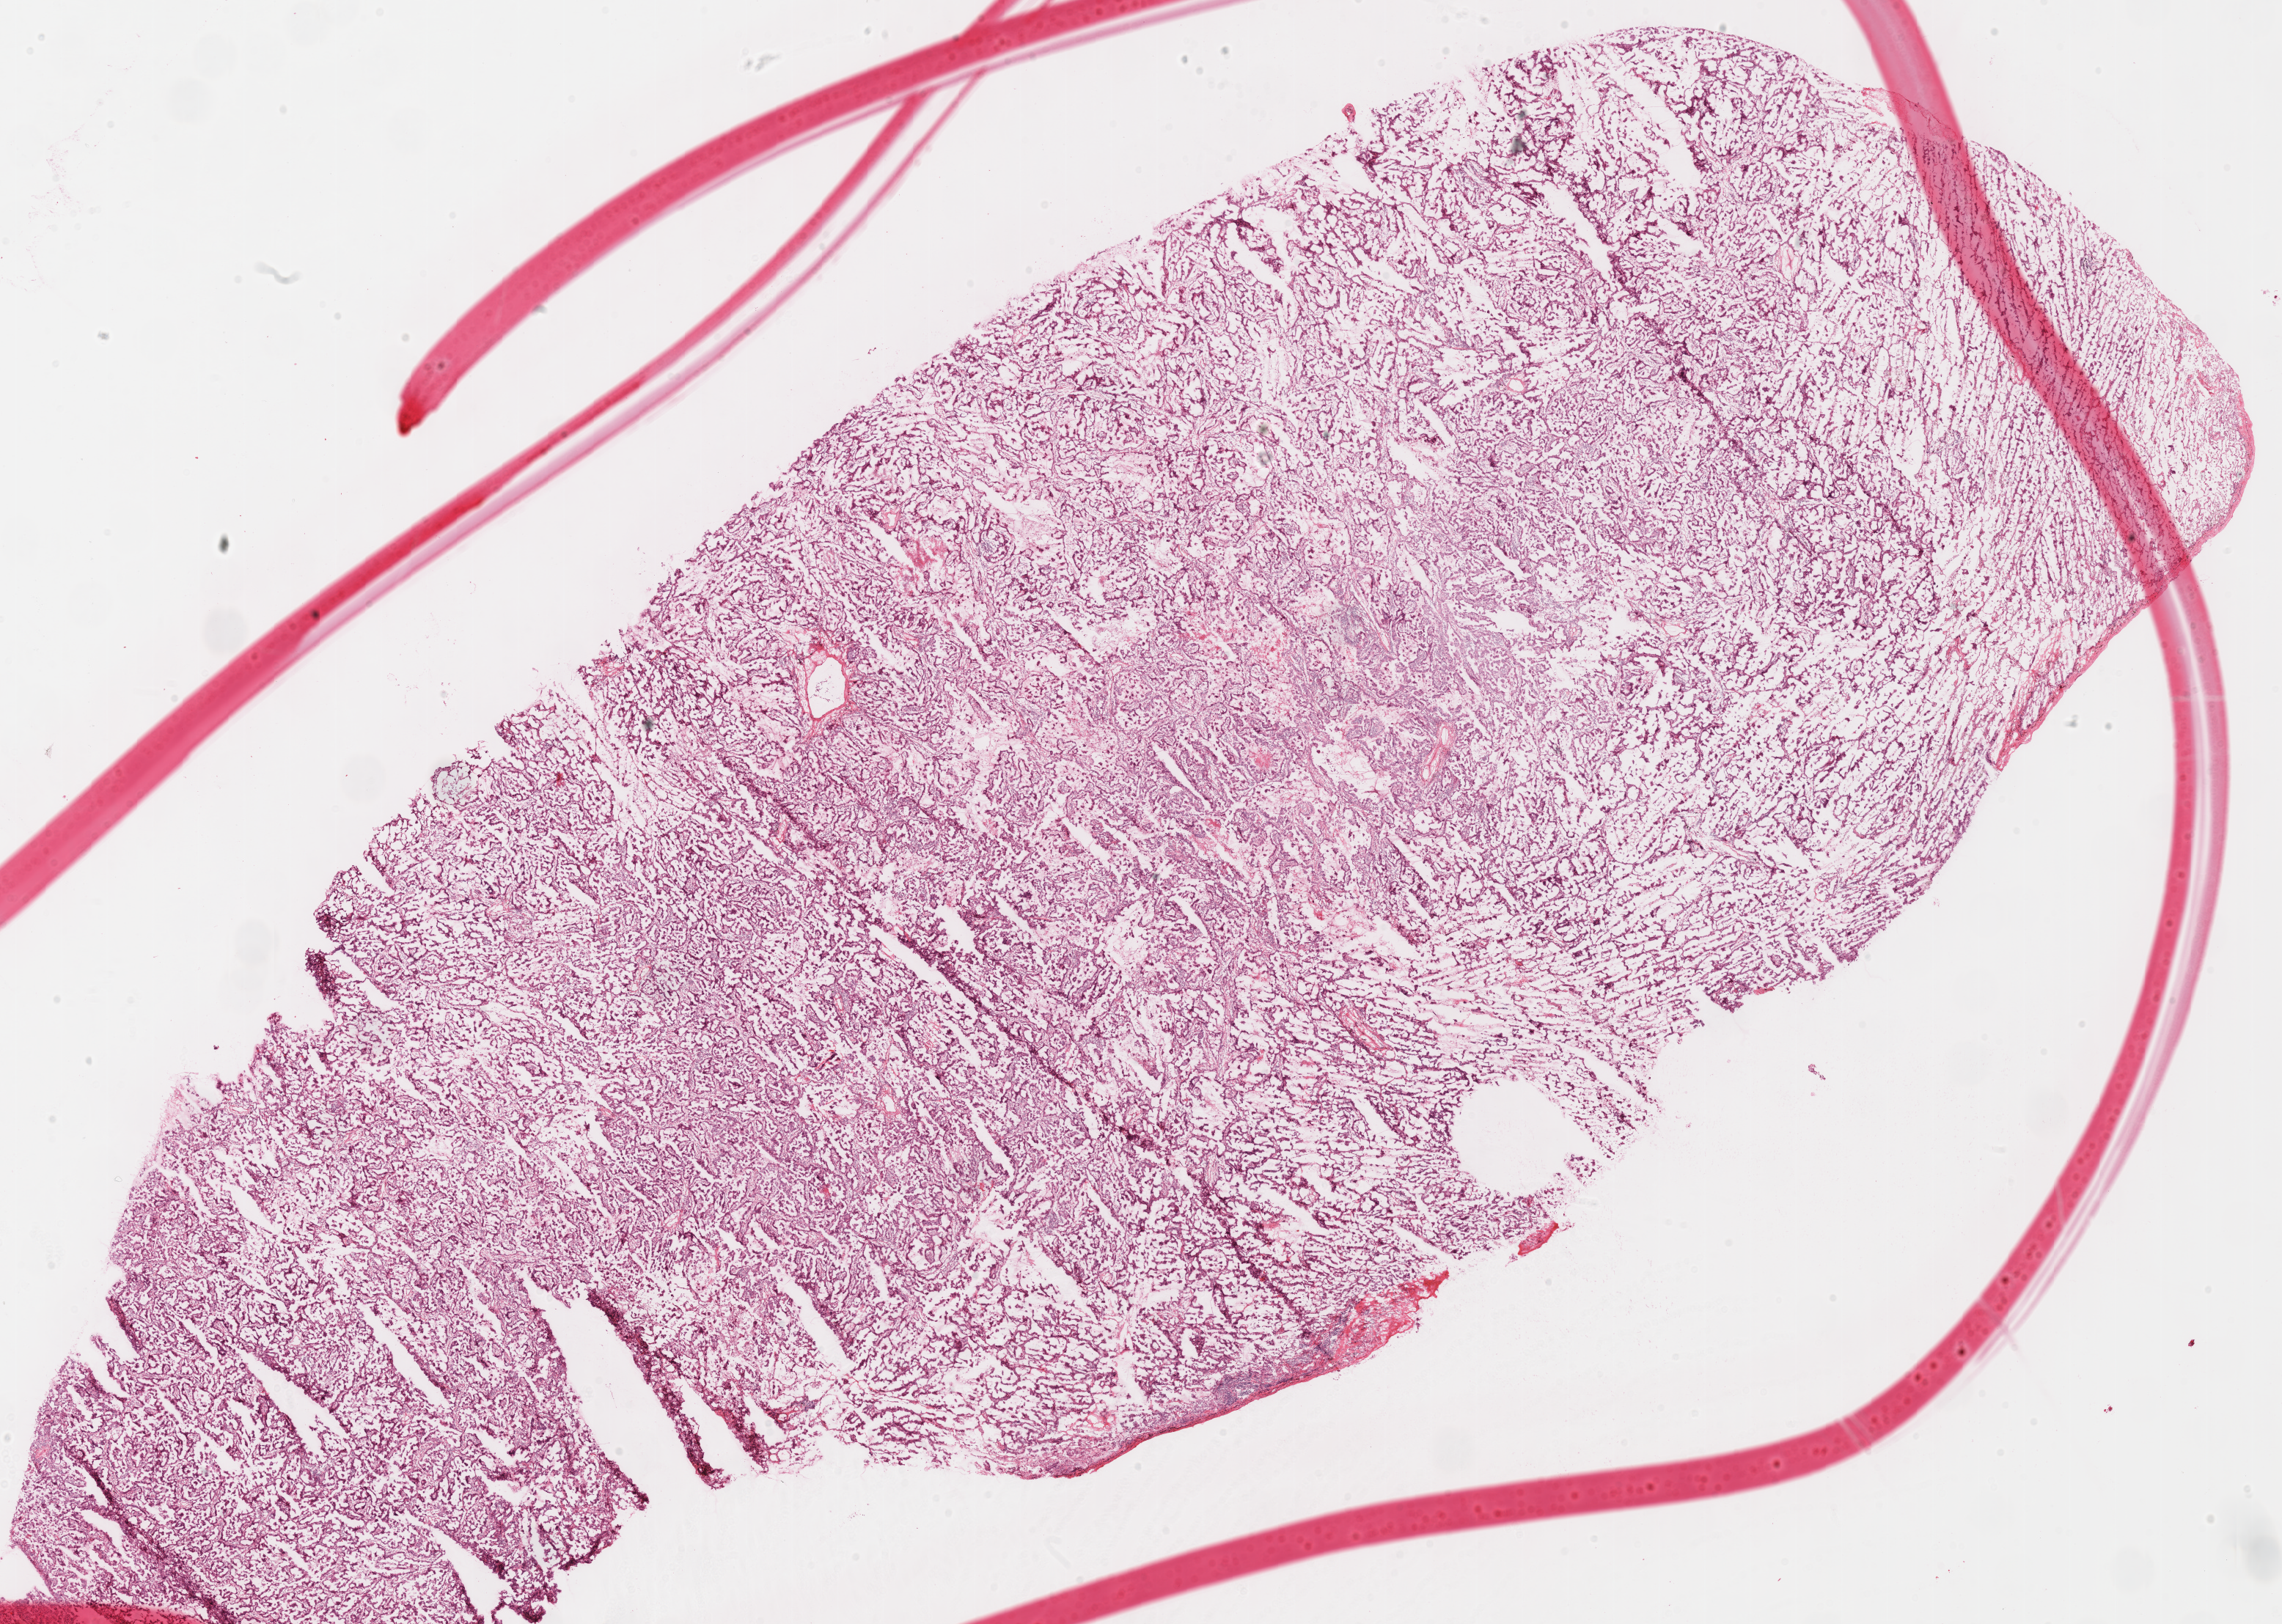
Digitized H&E-stained tissue section (whole slide), whole scanned area (about 24.5 x 17.4 mm) shown as a low-resolution overview. Frozen section. Sample: primary tumour, lung. Male, age 70 years at initial diagnosis. Slide review estimates, as recorded: tumour cells 100%, tumour nuclei 70%, normal cells 0%, stromal cells 0%, necrosis 0%. Inflammatory infiltration, as recorded: lymphocyte infiltration 10%, monocyte infiltration 5%, neutrophil infiltration 0%.
TNM: T2b N0 M0. AJCC pathologic stage: IIA. Pathologic diagnosis: Adenocarcinoma, NOS (middle lobe, lung). Laterality: right.